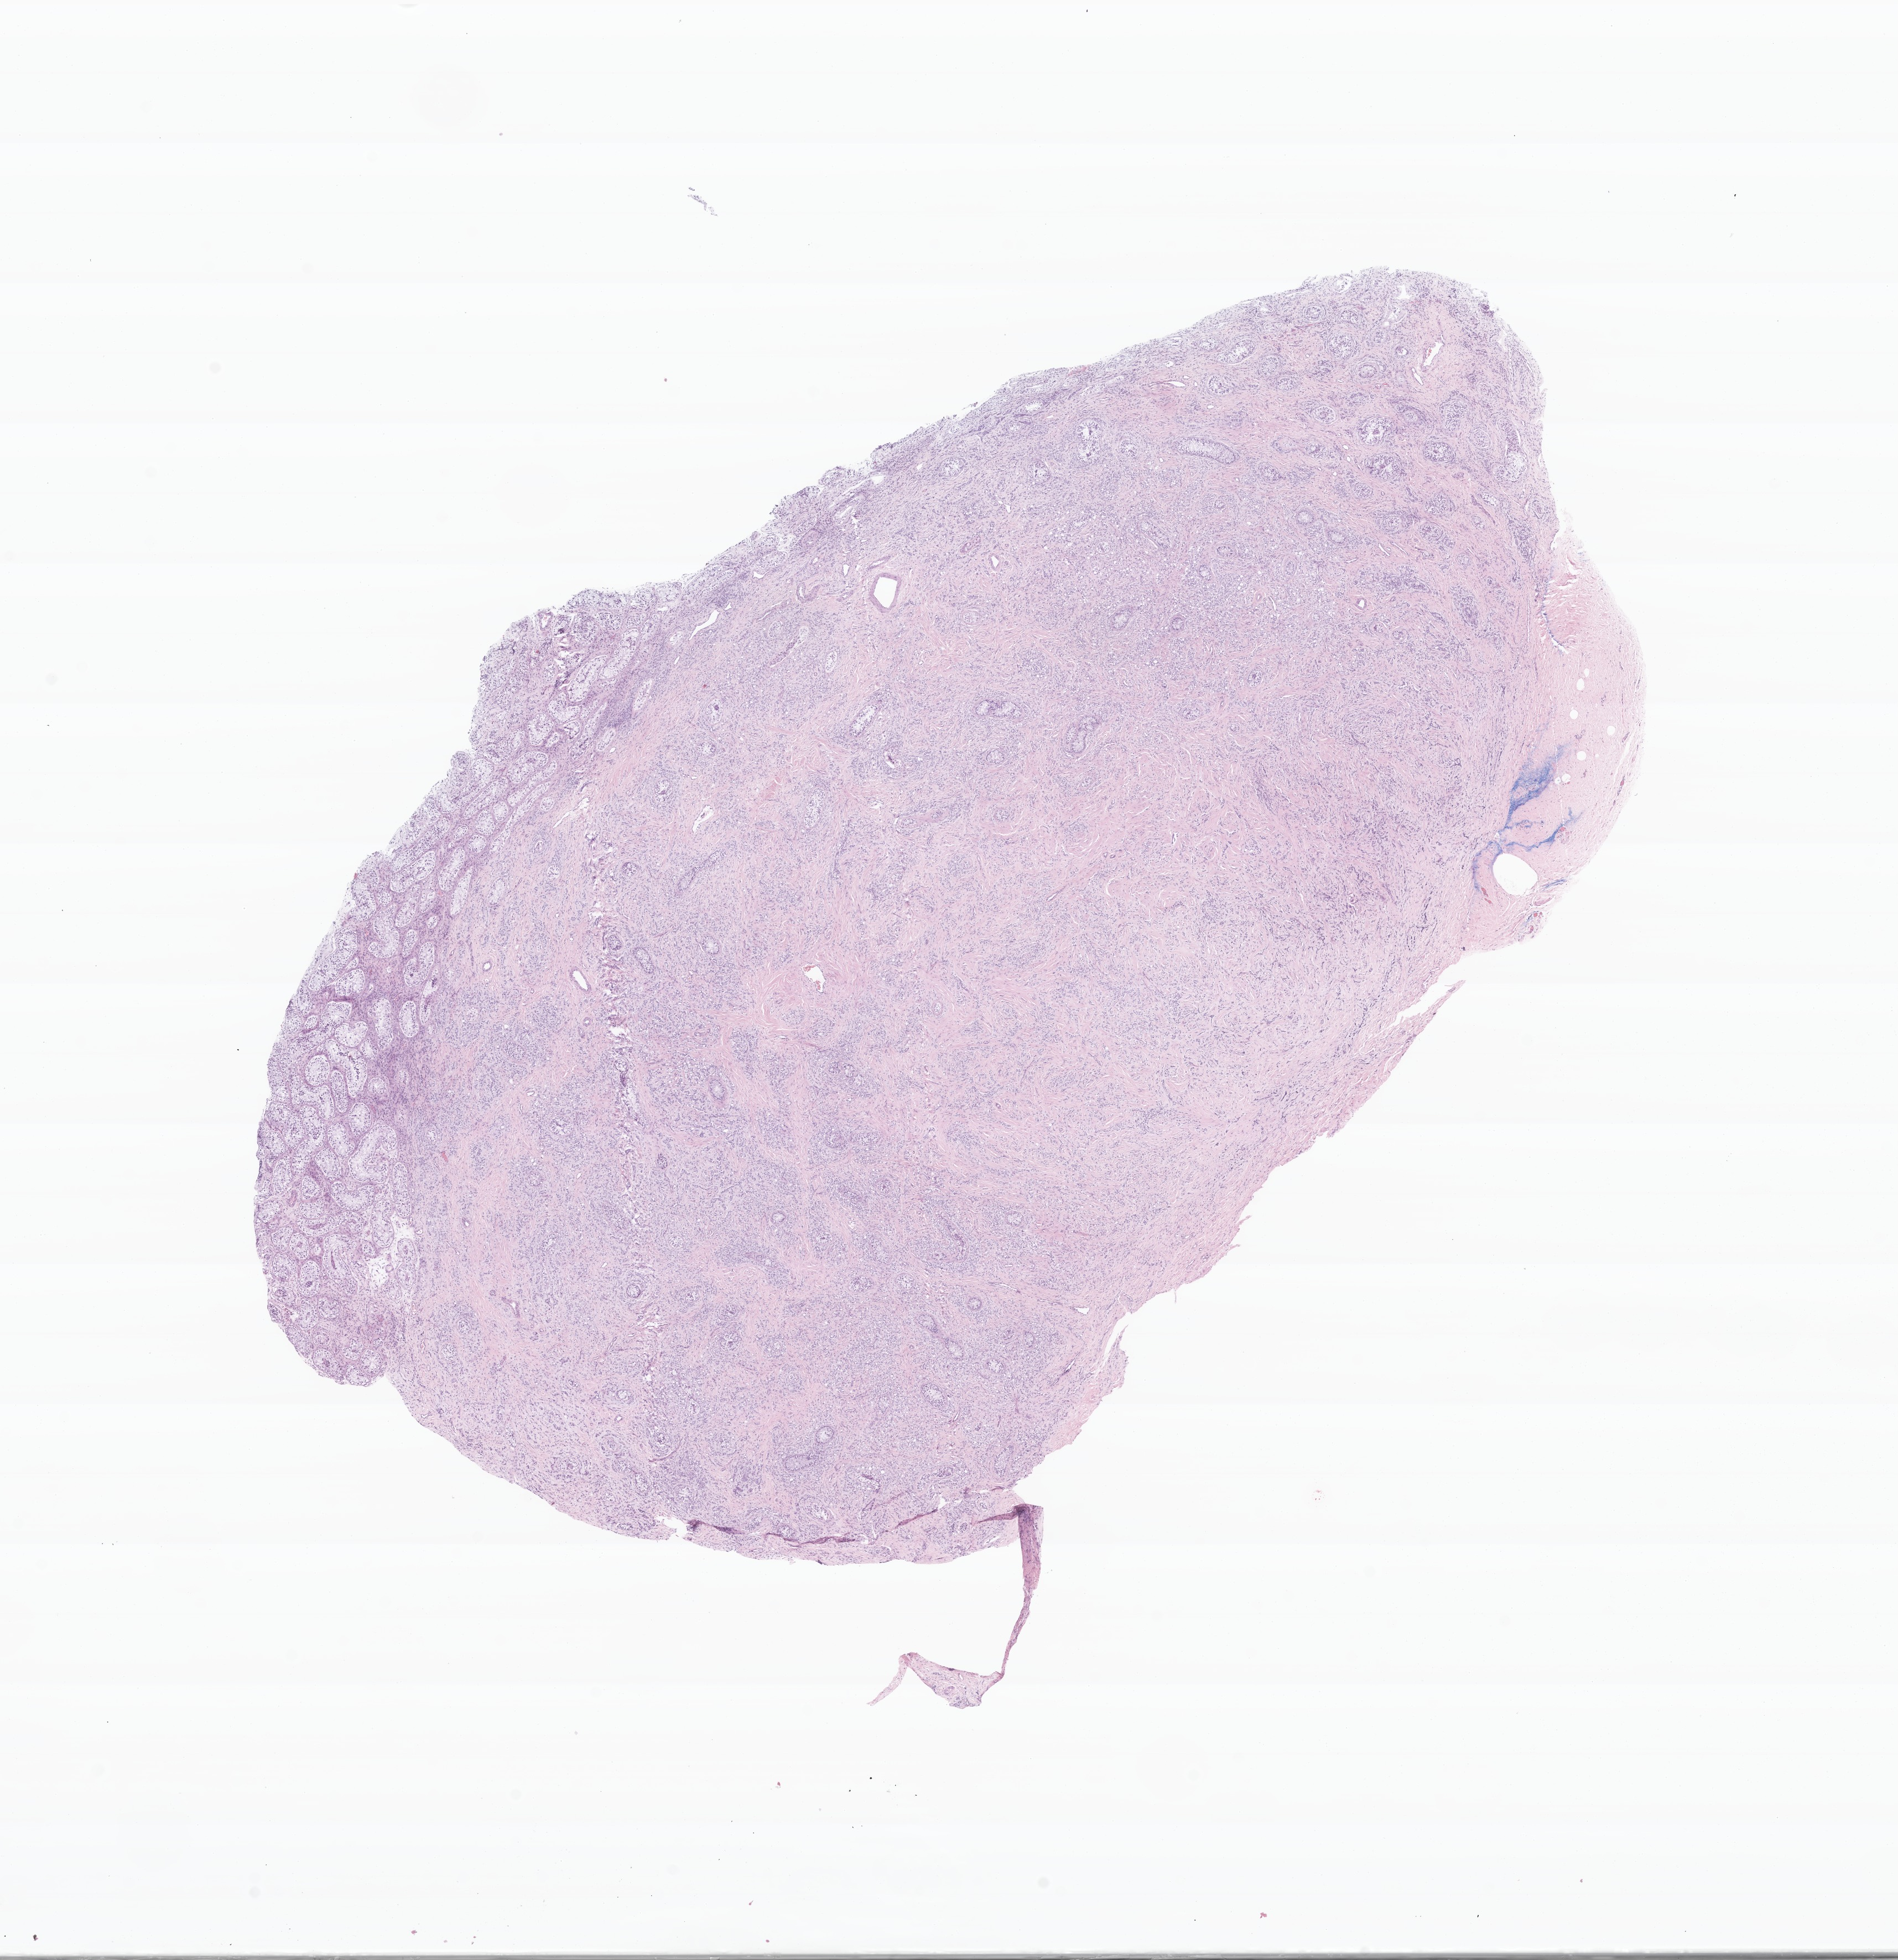
Digitized hematoxylin and eosin (H&E)-stained section of tumor tissue from the testis, whole scanned area (about 14.4 x 14.9 mm) shown as a low-resolution overview; formalin-fixed, paraffin-embedded (FFPE) tissue. Patient male; age 217 months (18 years 1 month).
Diagnosis: Sertoli cell tumor, NOS.